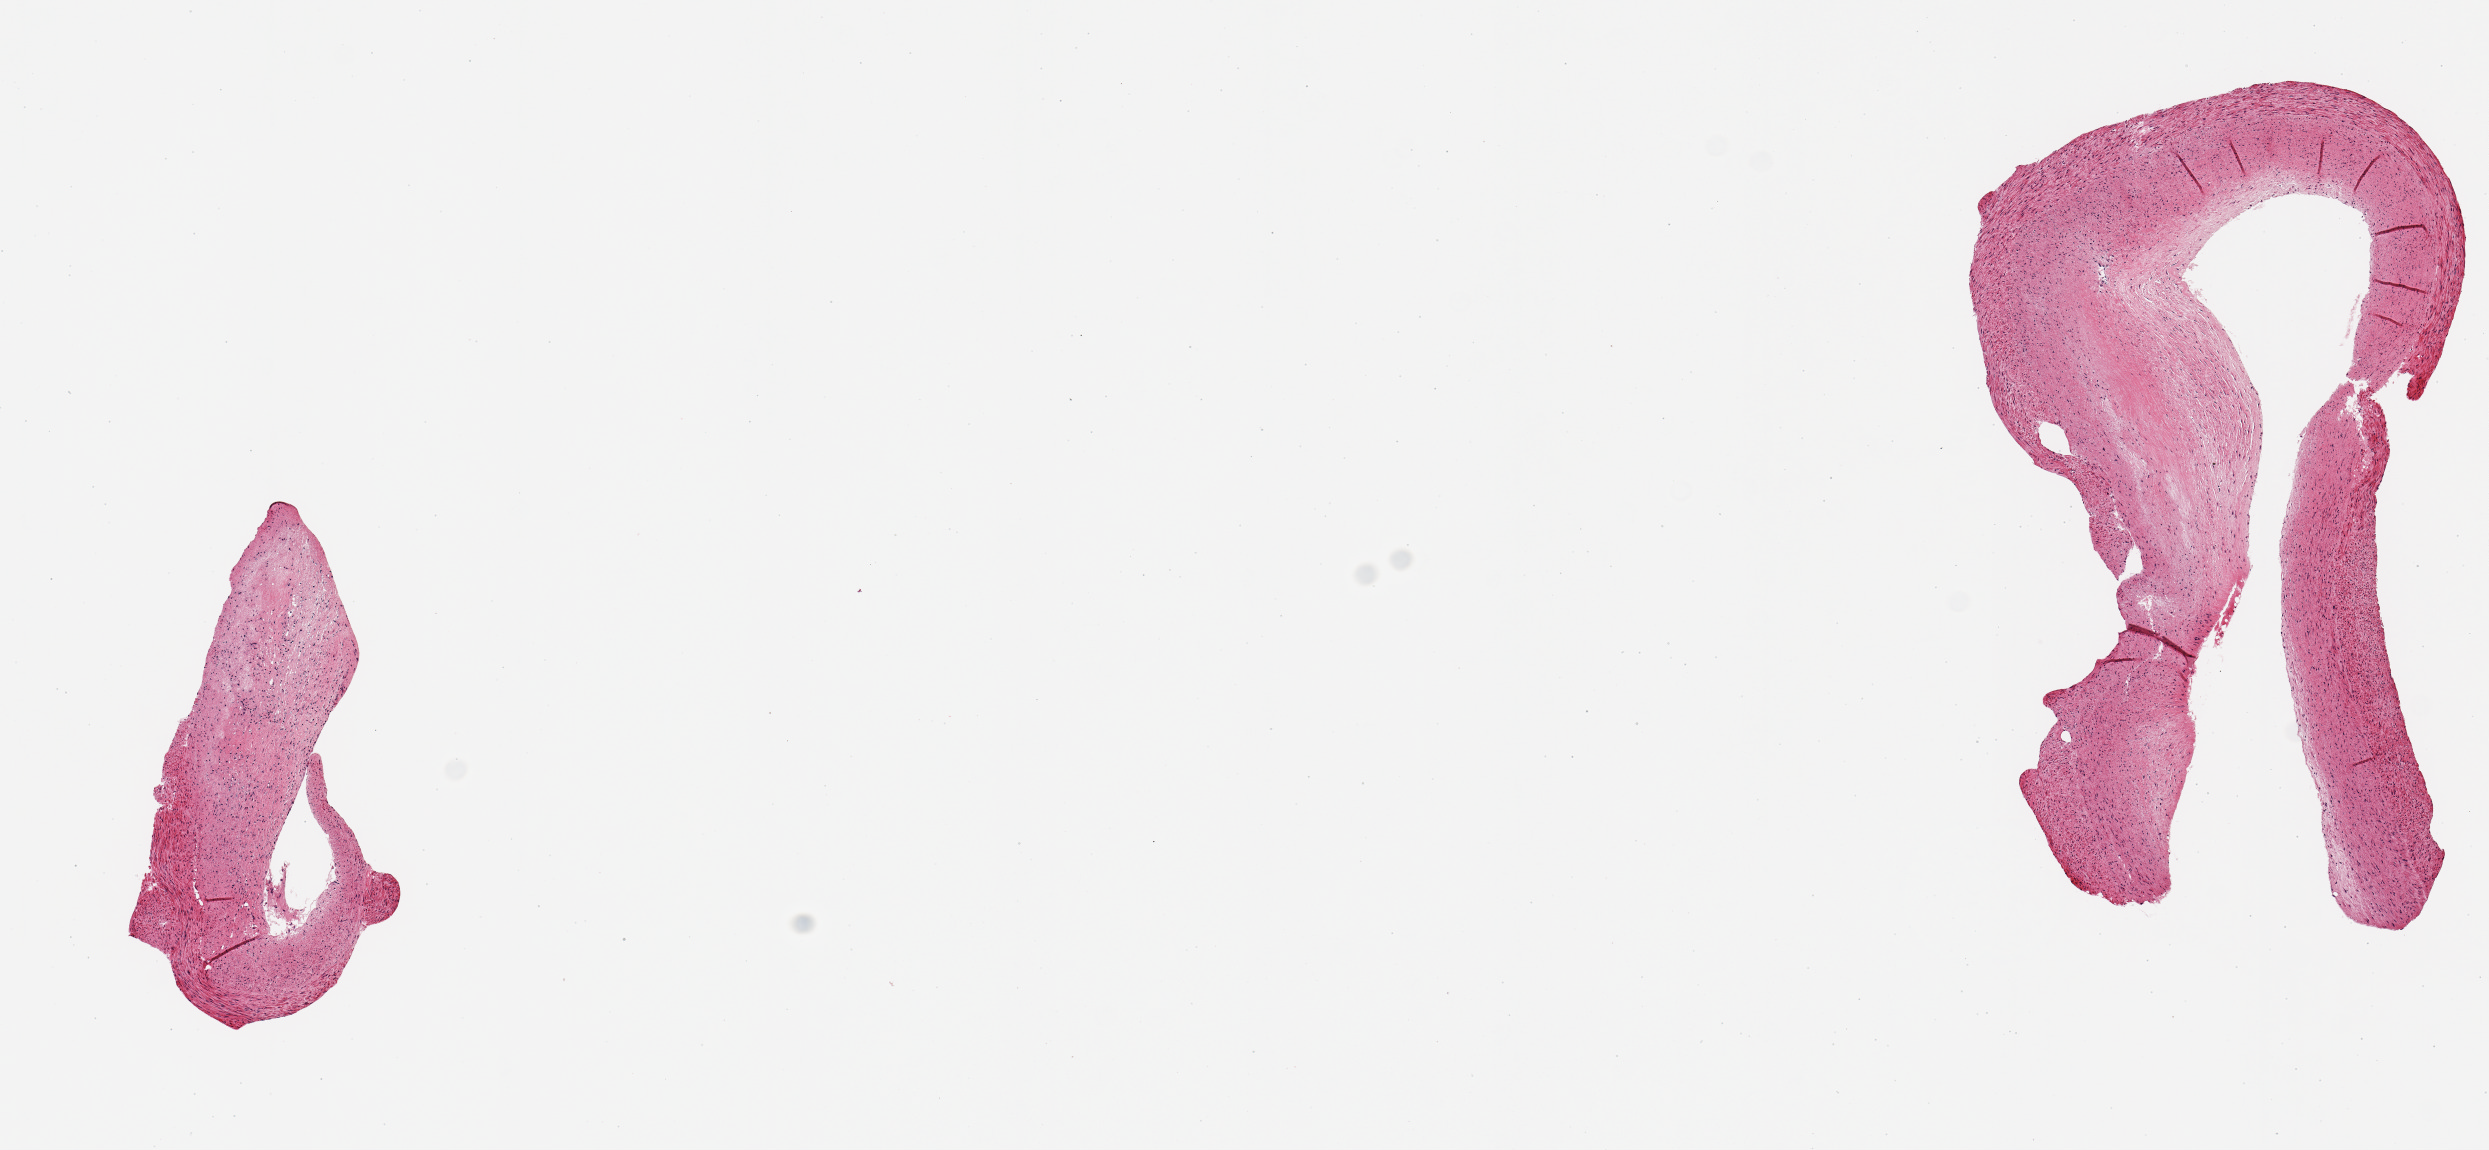
Digitized H&E-stained section, whole scanned area (about 9.8 x 4.5 mm, acquisition: 20x scan) shown as a low-resolution overview; PAXgene-fixed paraffin-embedded (PFPE) section; target tissue: coronary artery; tissue donor sample.
Review note (as recorded): 2 pieces (fragmented) ~30% occlusive atherosis.